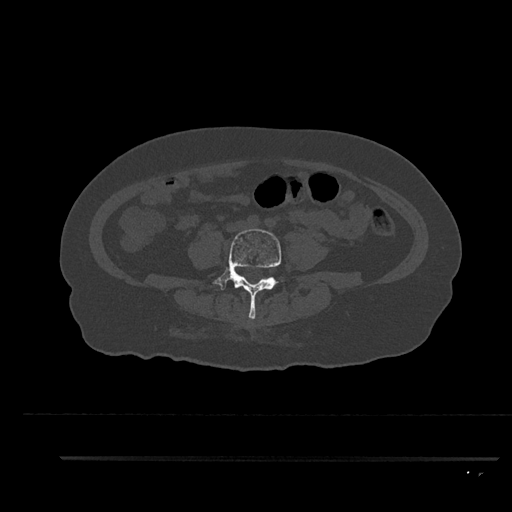
CT including the spine, one axial slice; slice 17 of 797 in the series (ordered by position); reconstruction kernel Br40s/3; 120 kVp; bone window (W 1800 / L 400 HU); 0.5 mm slice thickness; 512 × 512 image matrix. Patient: female, 44 years. Case-level facts recorded for this patient, not image findings: primary cancer: renal; vertebrae with lytic lesions (as recorded): L1.
Outlined on this slice (semi-automatic segmentation, software-assisted and operator-edited):
- L4 vertebra: box from (x=210, y=229) to (x=283, y=319) px